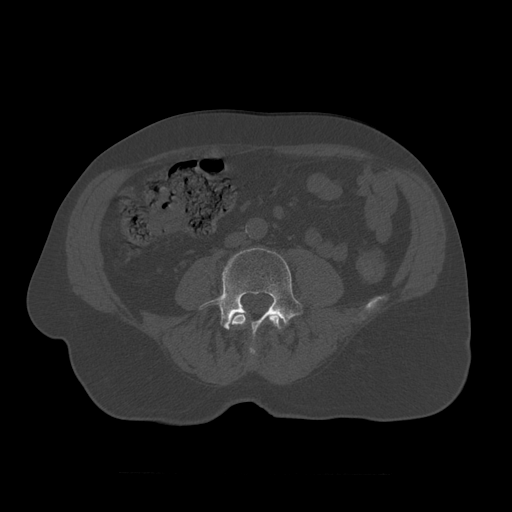
CT including the spine, one axial slice; slice 282 of 450 in the series (ordered by position); reconstruction kernel STANDARD; 120 kVp; bone window (W 1800 / L 400 HU); 1.25 mm slice thickness; 512 × 512 image matrix, field of view 405 × 405 mm. Patient age 75 years. From the clinical record (not read from this slice): primary cancer: prostate.
Annotated regions visible in this slice (semi-automatic segmentation, software-assisted and operator-edited):
- L3 vertebra: bounding box <230,312,283,355> (left, top, right, bottom; pixels)
- L4 vertebra: <200,248,304,339>